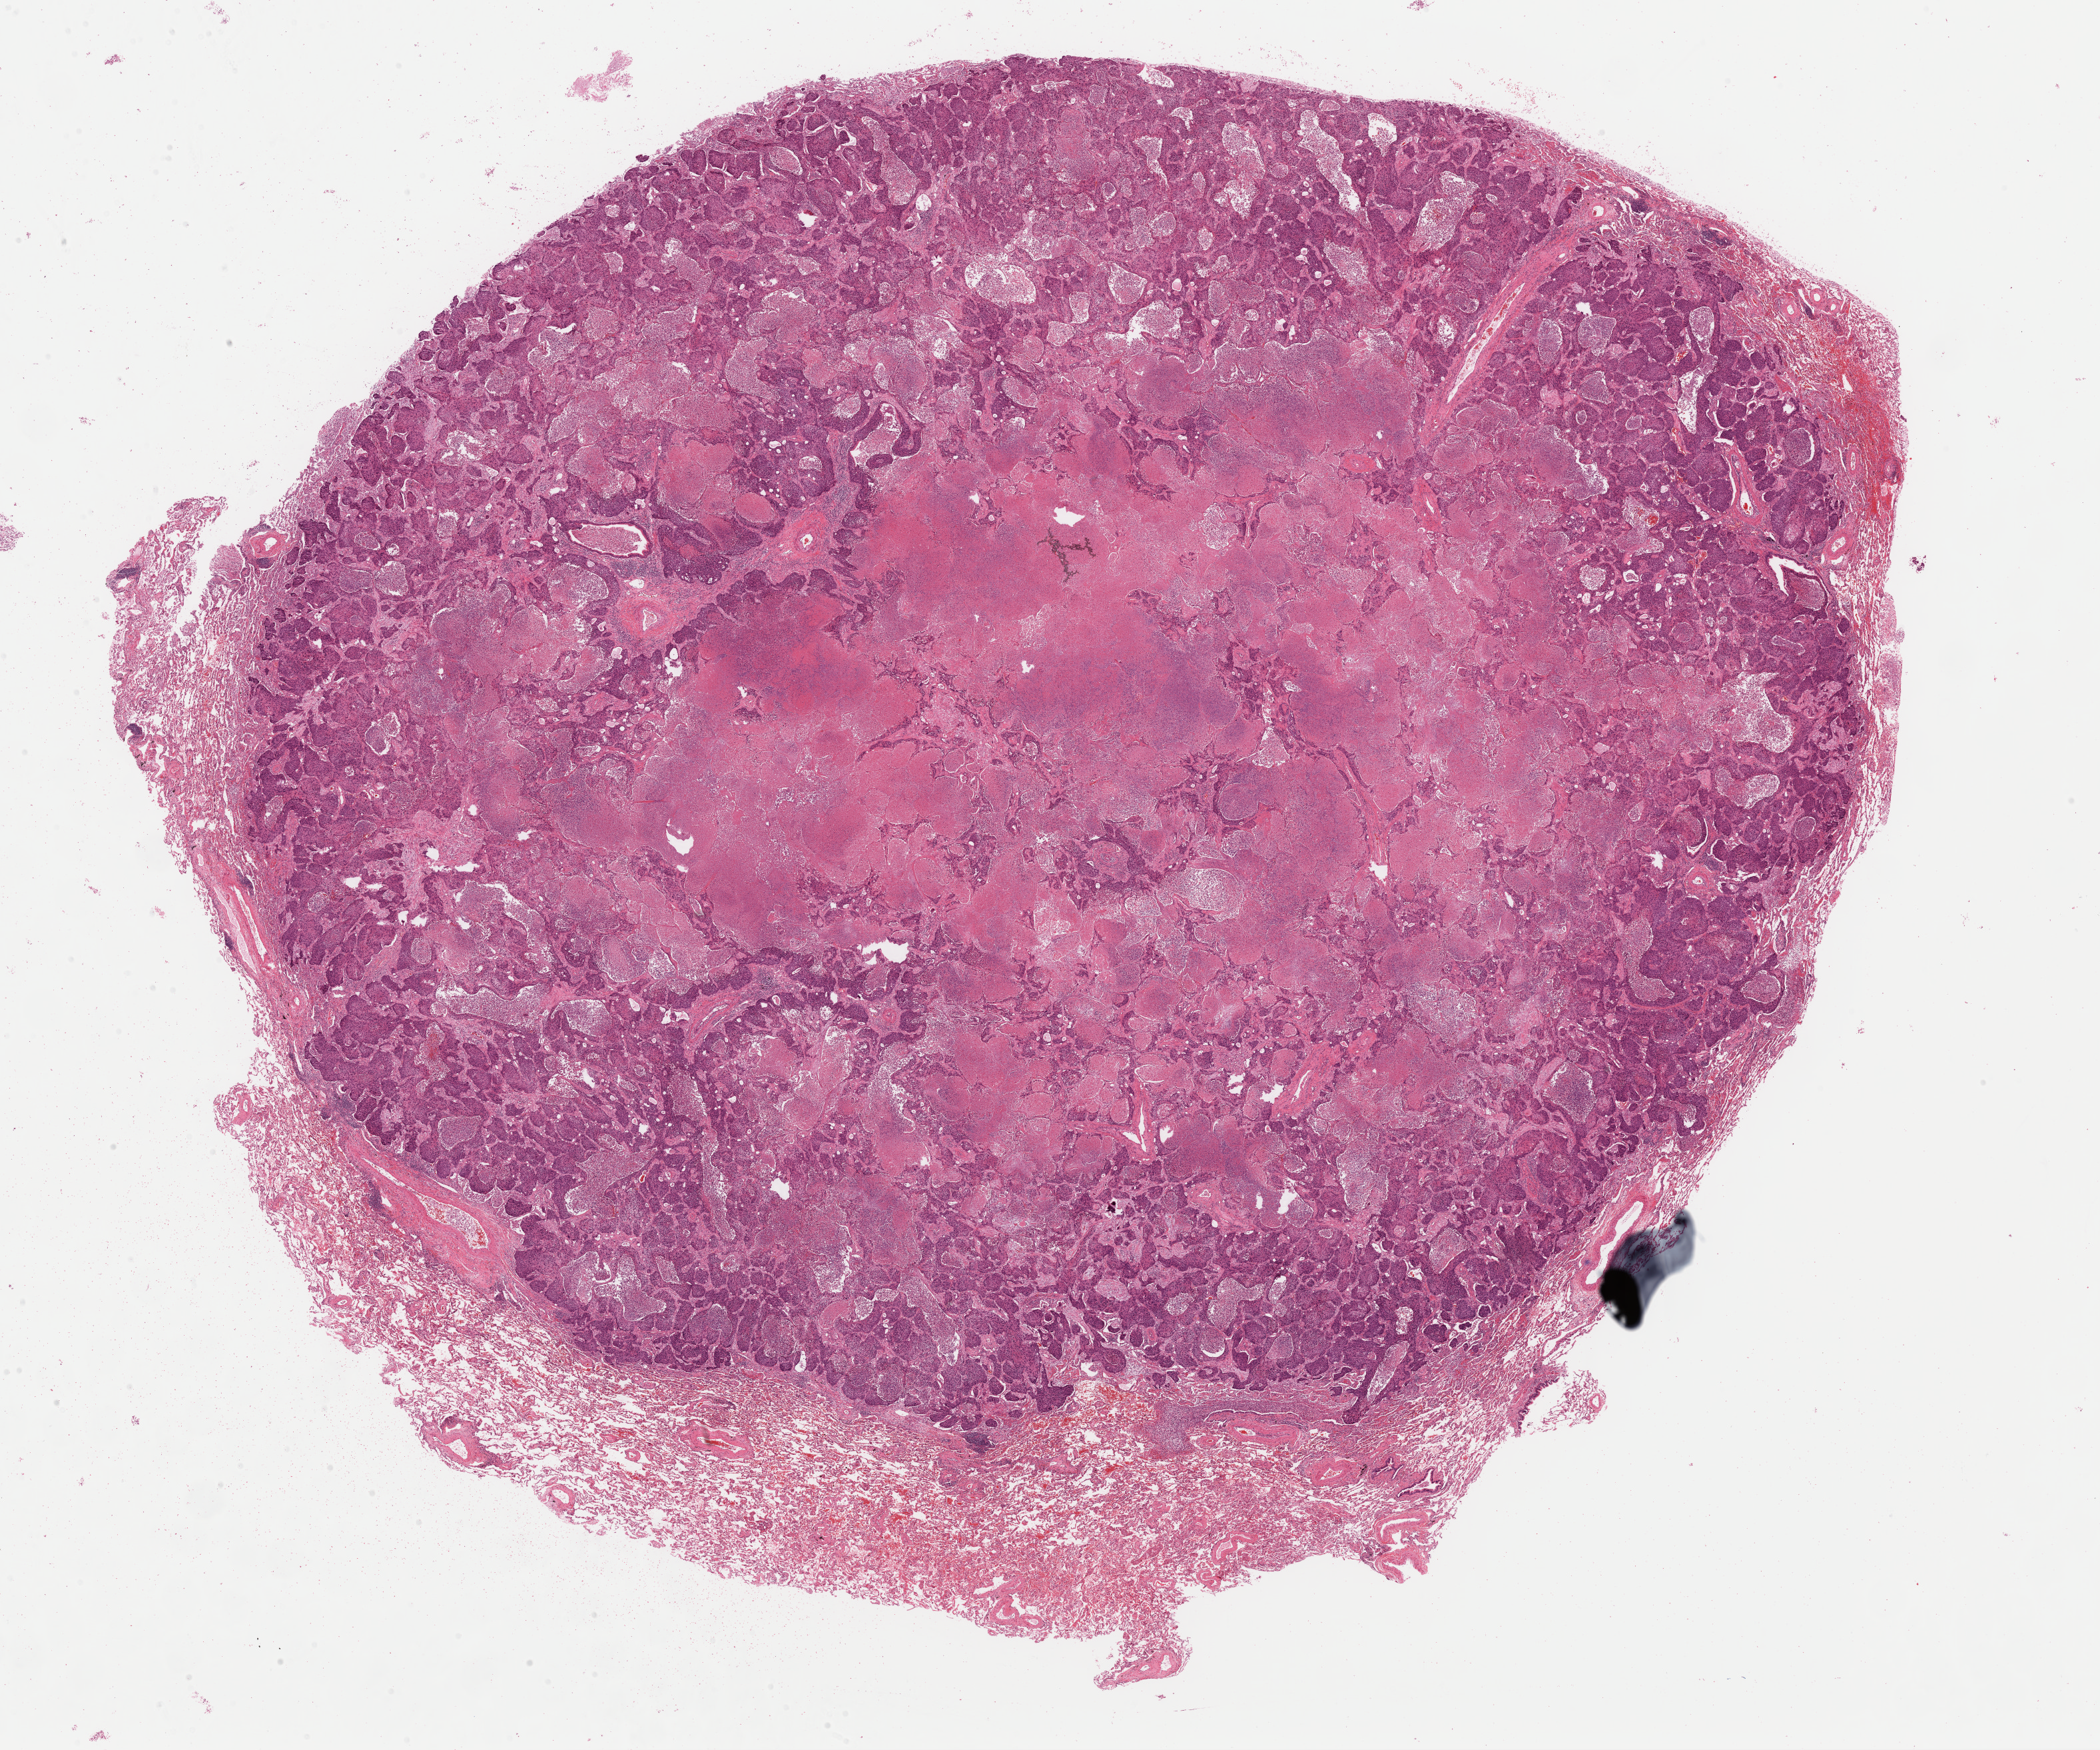
Whole-slide histology image, Hematoxylin and eosin (H&E) stained, whole scanned area (about 24.9 x 20.8 mm) shown as a low-resolution overview, formalin-fixed paraffin-embedded (FFPE) diagnostic section, lung, primary tumour sample. Patient: female, age at initial diagnosis 74 years.
AJCC pathologic stage: IB. Diagnosis: Squamous cell carcinoma, NOS (lower lobe, lung).